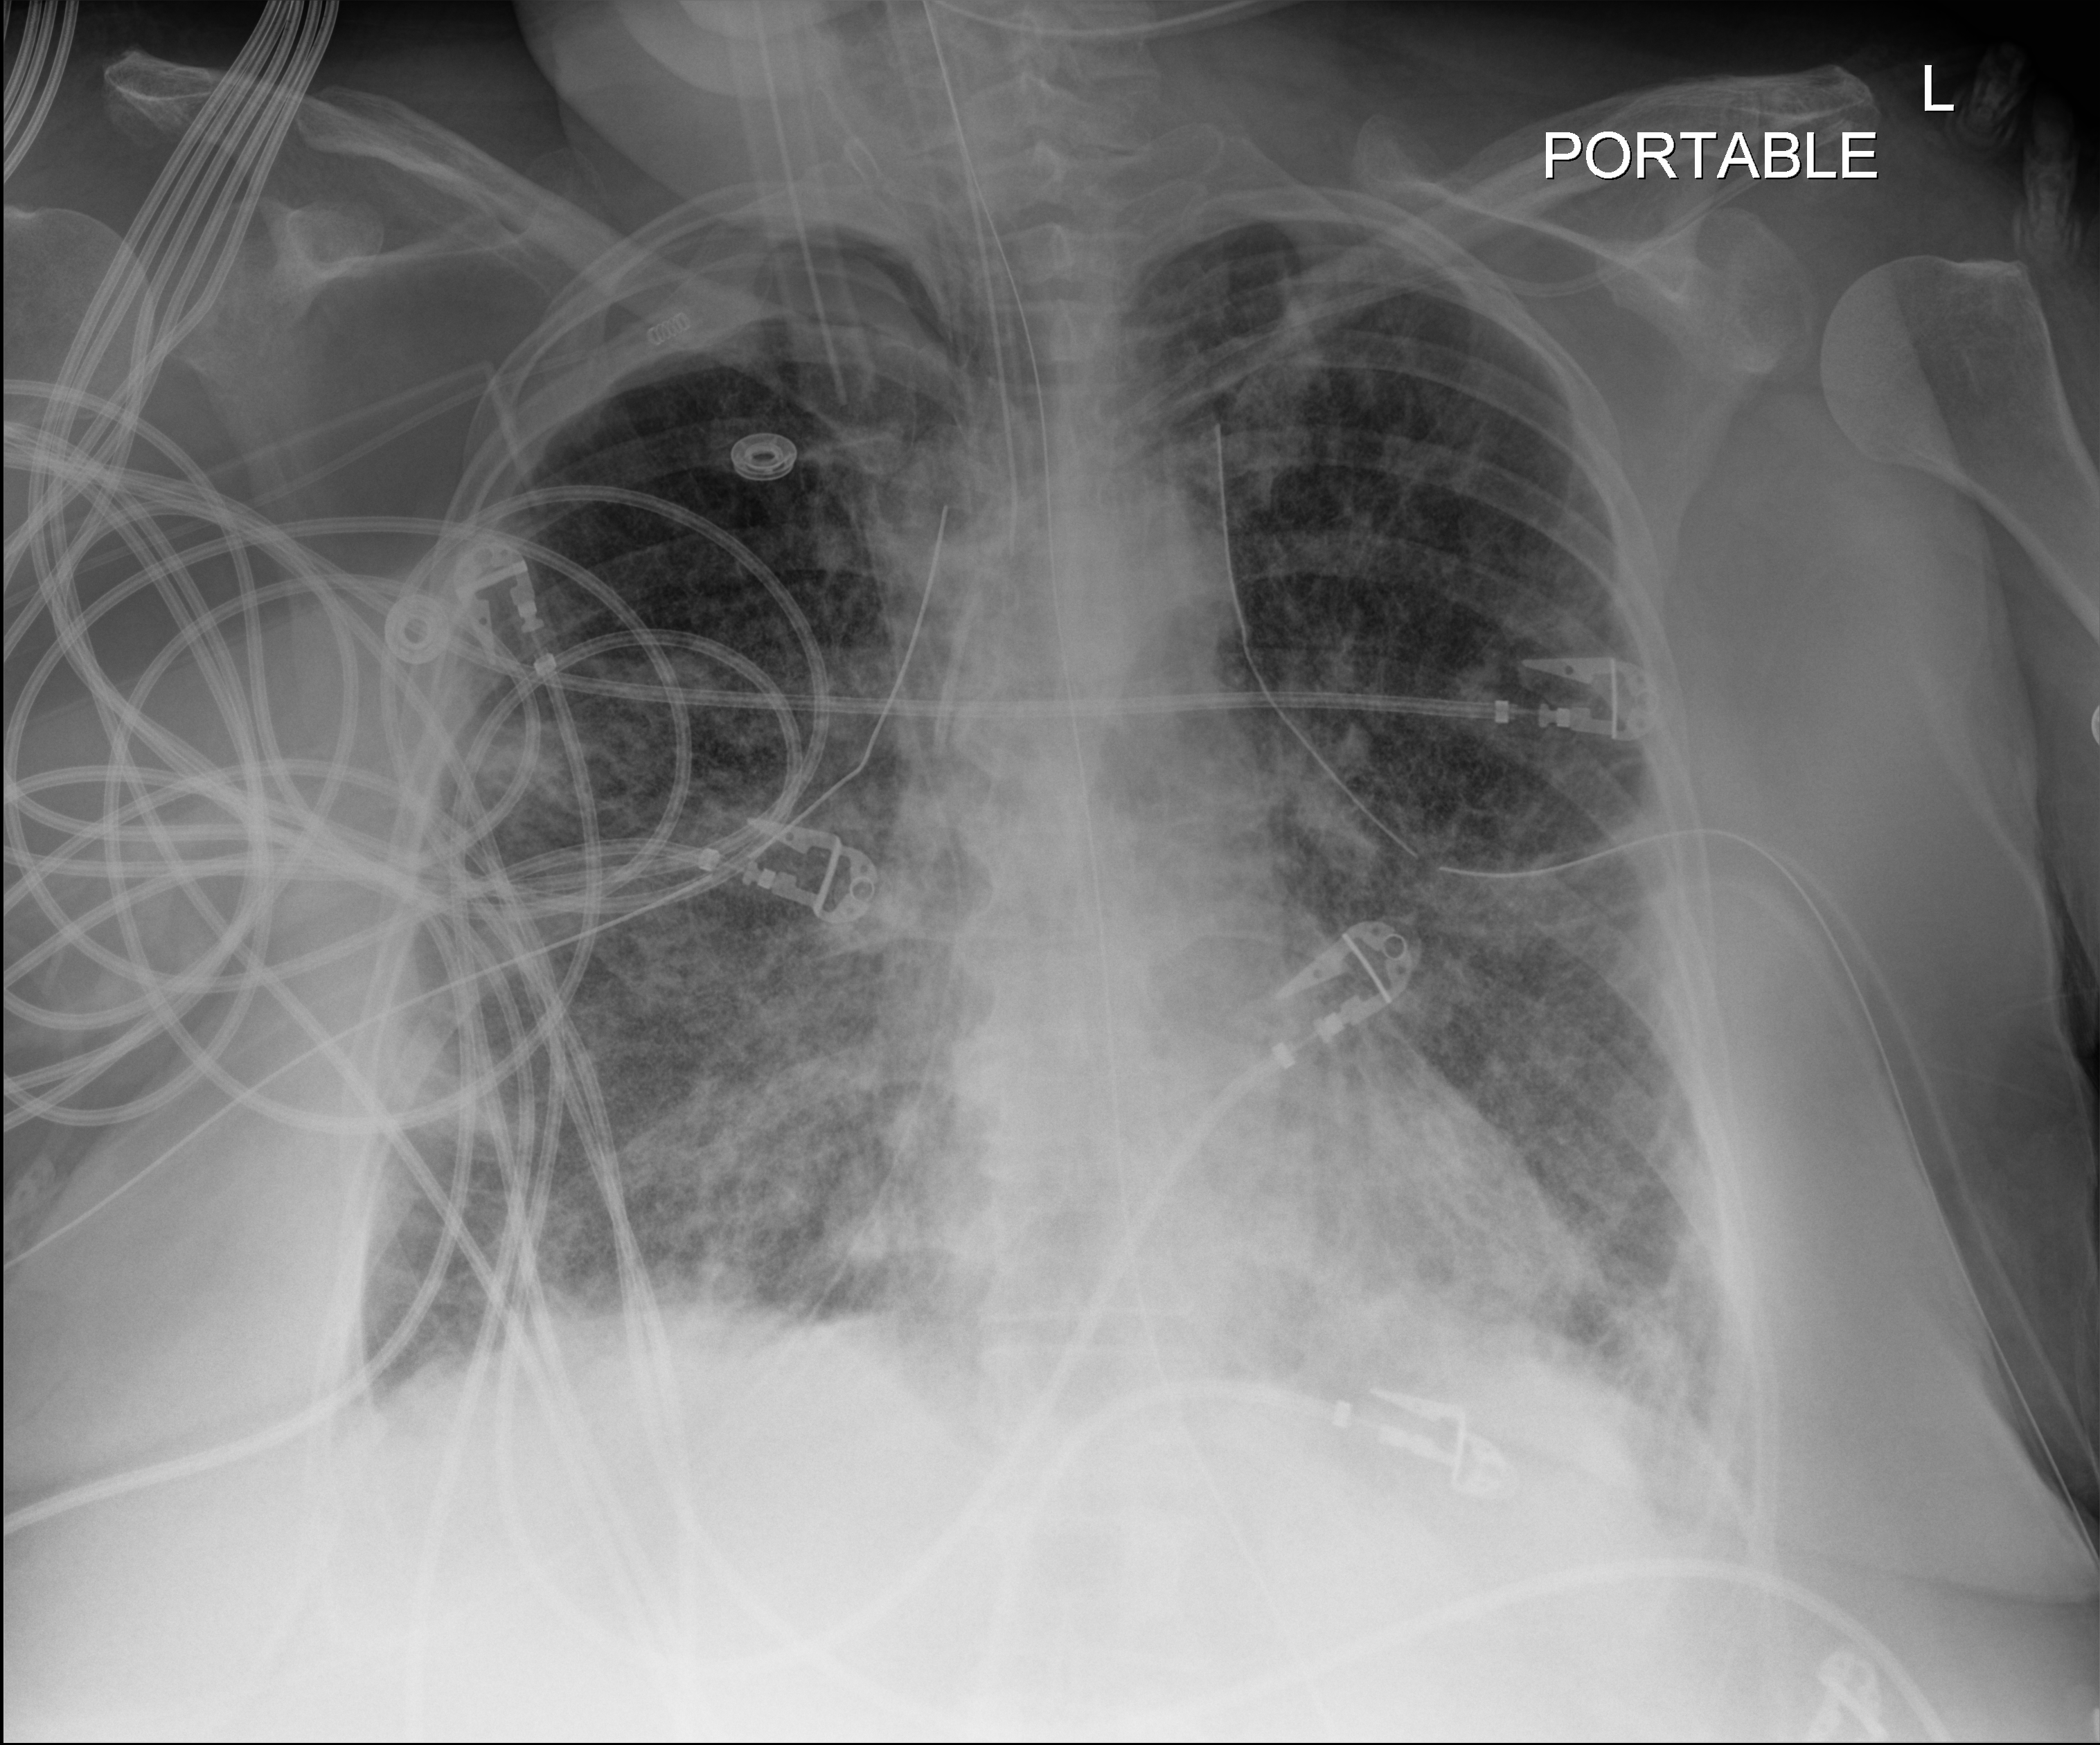
Portable chest radiograph, anteroposterior (AP) projection. Patient hospitalised with COVID-19; female, aged 60–74 years.
From the hospital-stay record, not from the radiograph (when in the stay this image was taken is not recorded): mechanically ventilated during this hospital stay: yes; admitted to intensive care during this hospital stay: yes.